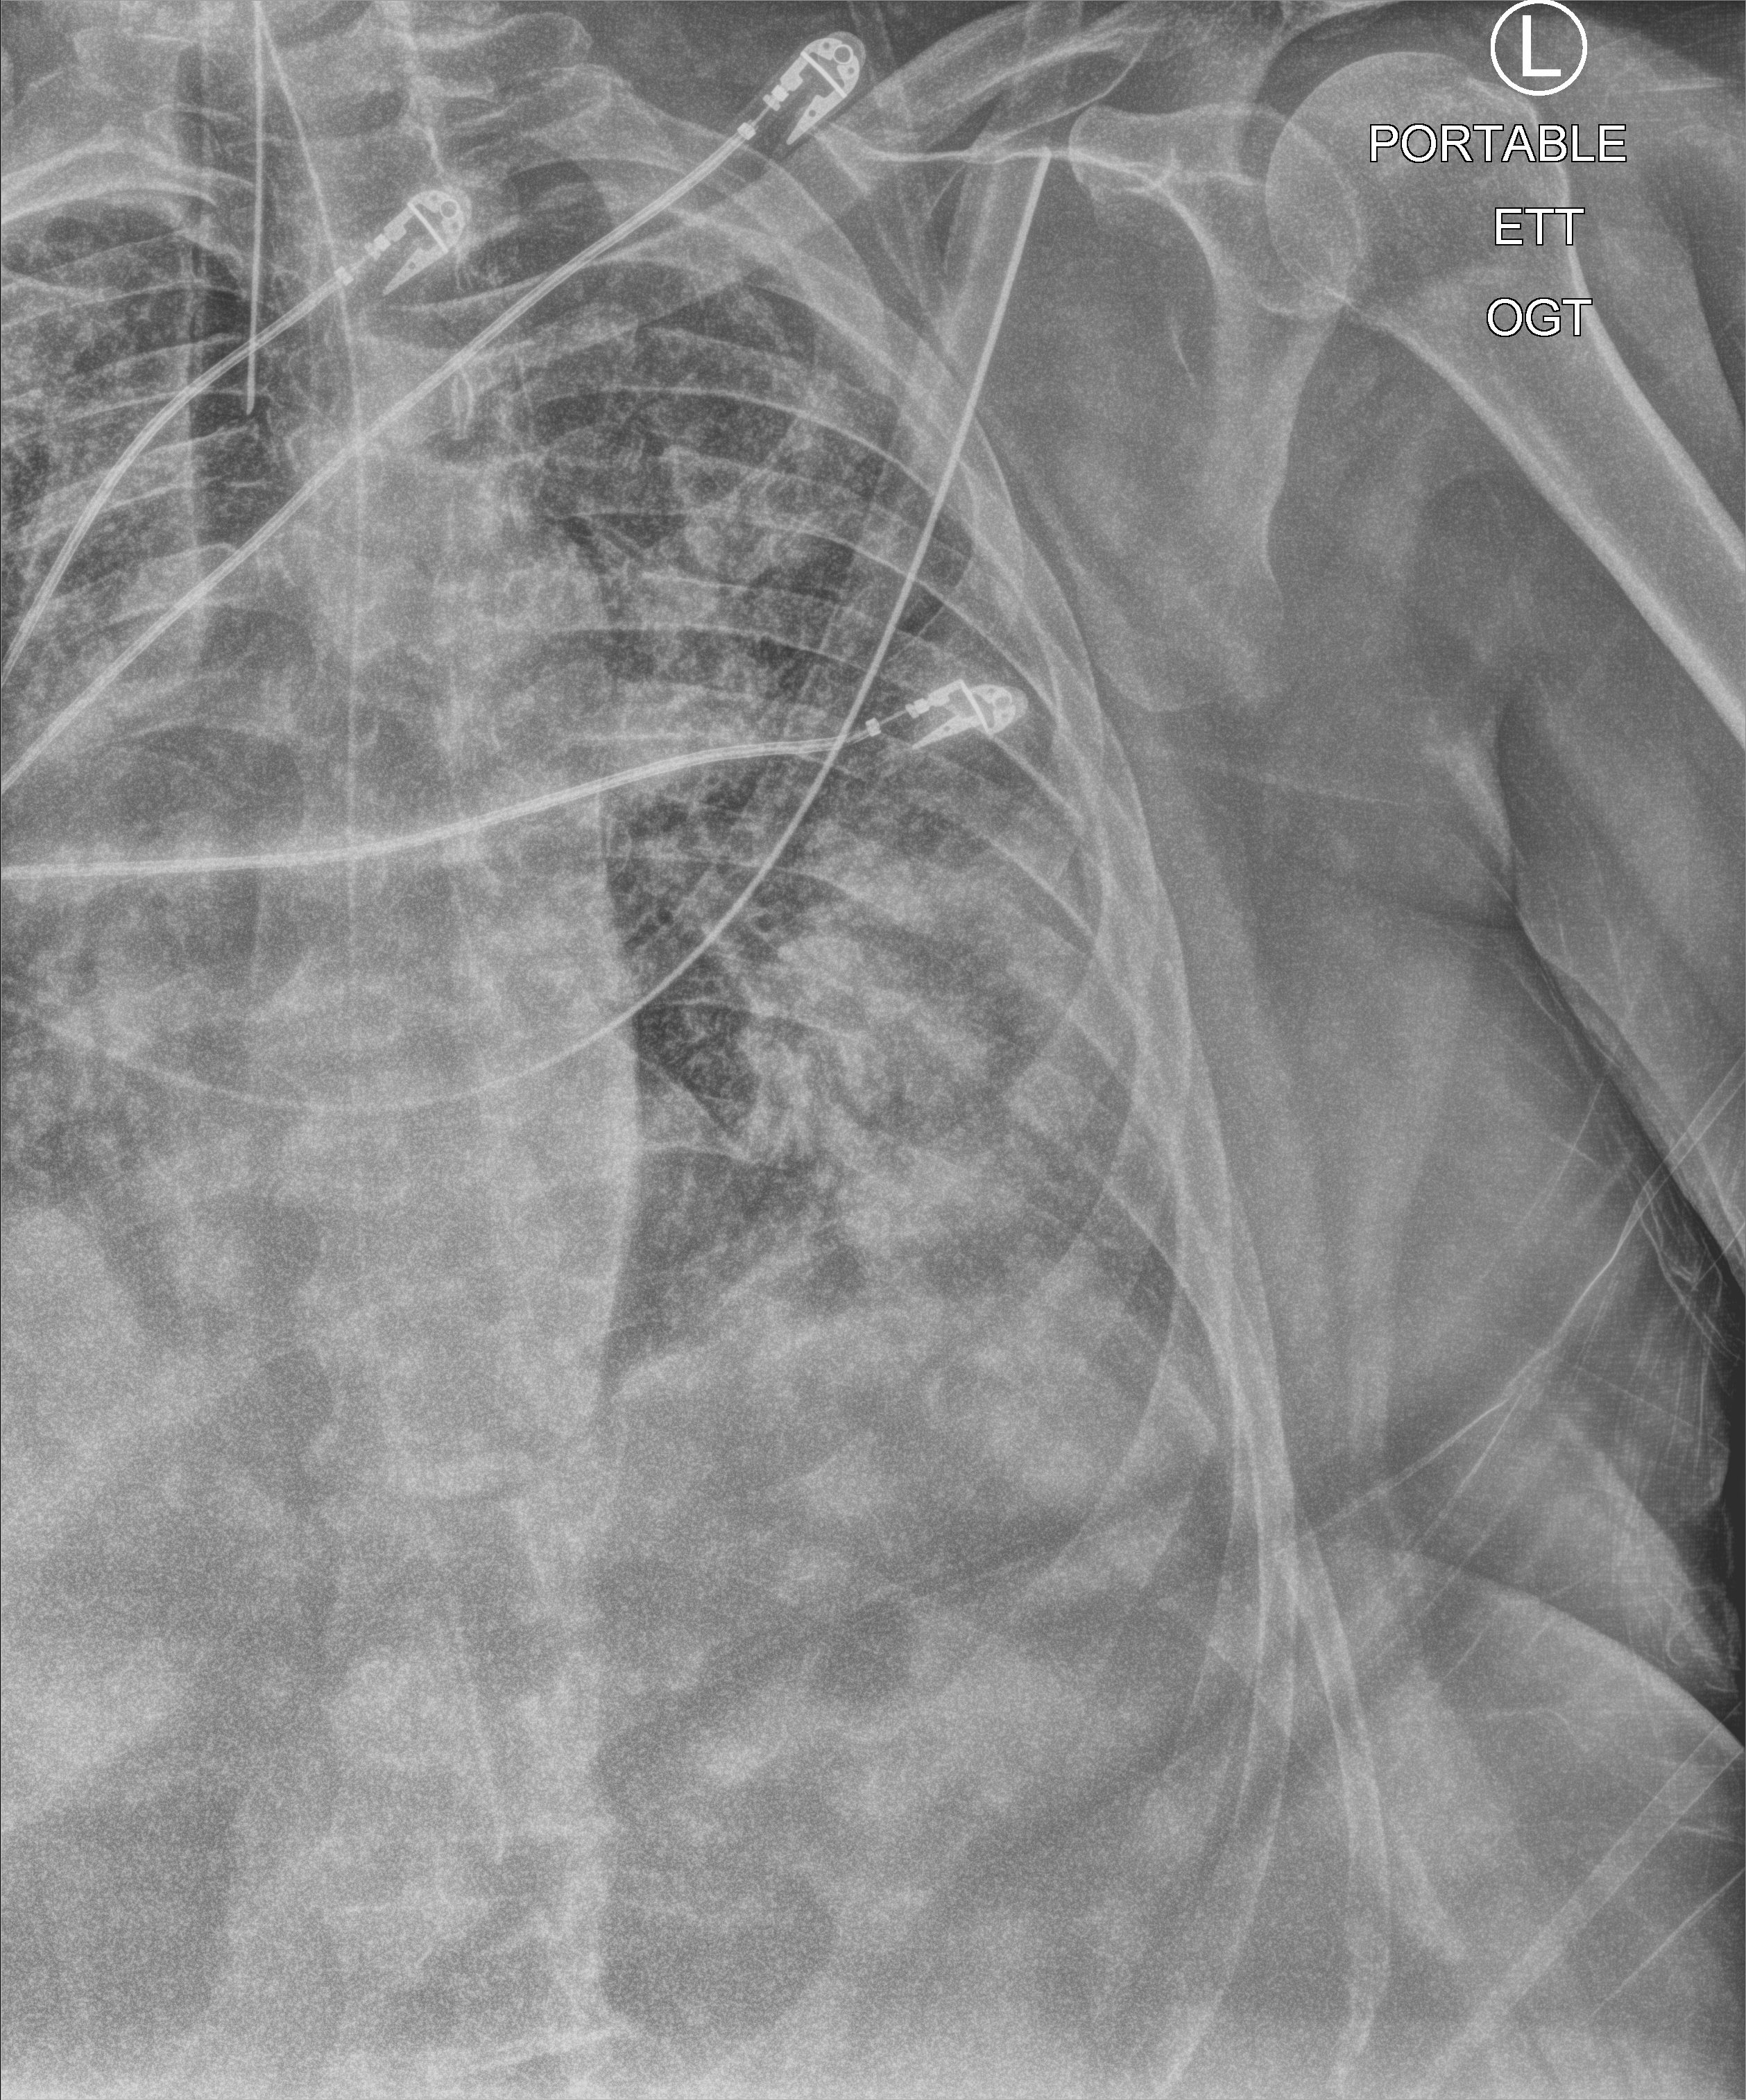
Chest X-ray (portable), anteroposterior (AP) projection. Patient hospitalised with COVID-19; male, aged 60–74 years.
From the hospital-stay record, not from the radiograph (when in the stay this image was taken is not recorded):
- smoking status (admission record): former
- mechanically ventilated during this hospital stay: yes